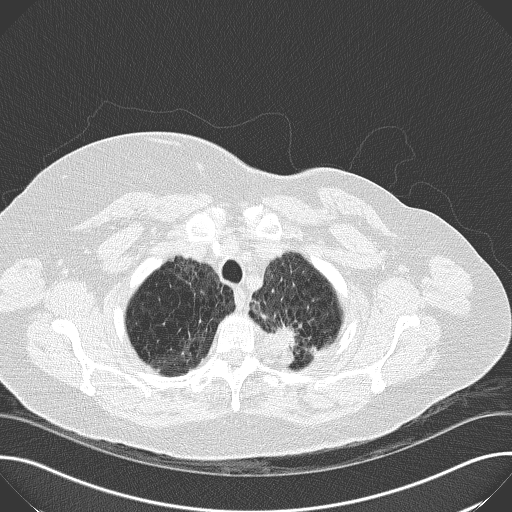
Axial slice from a low-dose chest CT screening exam, baseline annual screen, lung window (W 1500 / L -600 HU), 2 mm slice thickness, 512 × 512 image matrix, field of view 380 × 380 mm. Female, age 56 years at enrolment.
Lesion marked by an expert reader, bounding box <250,304,317,369> (left, top, right, bottom; pixels). Screening reader's record for this exam (one nodule recorded; not confirmed to be the boxed lesion): non-calcified nodule or mass ≥4 mm, left upper lobe, 19 × 17 mm, spiculated (stellate) margins, soft tissue attenuation. Later outcome: lung cancer diagnosed 70 days after this screen — mucin-producing adenocarcinoma, left upper lobe, well differentiated (G1), stage IIB (AJCC 6th edition), 30 mm at pathology.